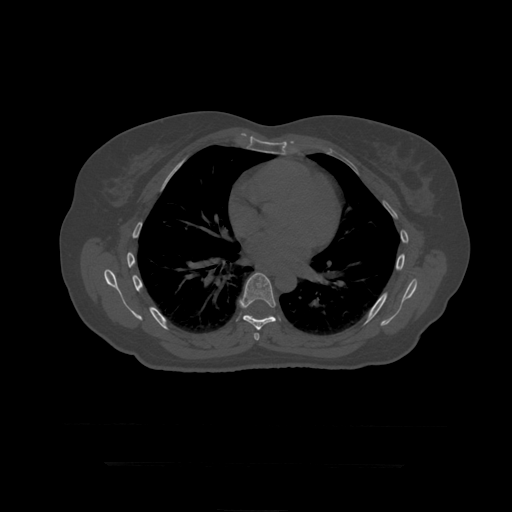
CT including the spine, one axial slice. Slice 280 of 399 in the series (ordered by position). Reconstruction kernel STANDARD. Bone window (W 1800 / L 400 HU). 1.25 mm slice thickness. 512 × 512 image matrix. Patient age 41 years. From the clinical record (not read from this slice): primary cancer: breast.
Annotated regions visible in this slice (semi-automatic segmentation, software-assisted and operator-edited):
- T7 vertebra: bounding box (x1, y1, x2, y2) in pixels: (254, 333, 260, 341)
- T8 vertebra: (240, 273, 276, 330)
- T9 vertebra: (245, 315, 249, 316)